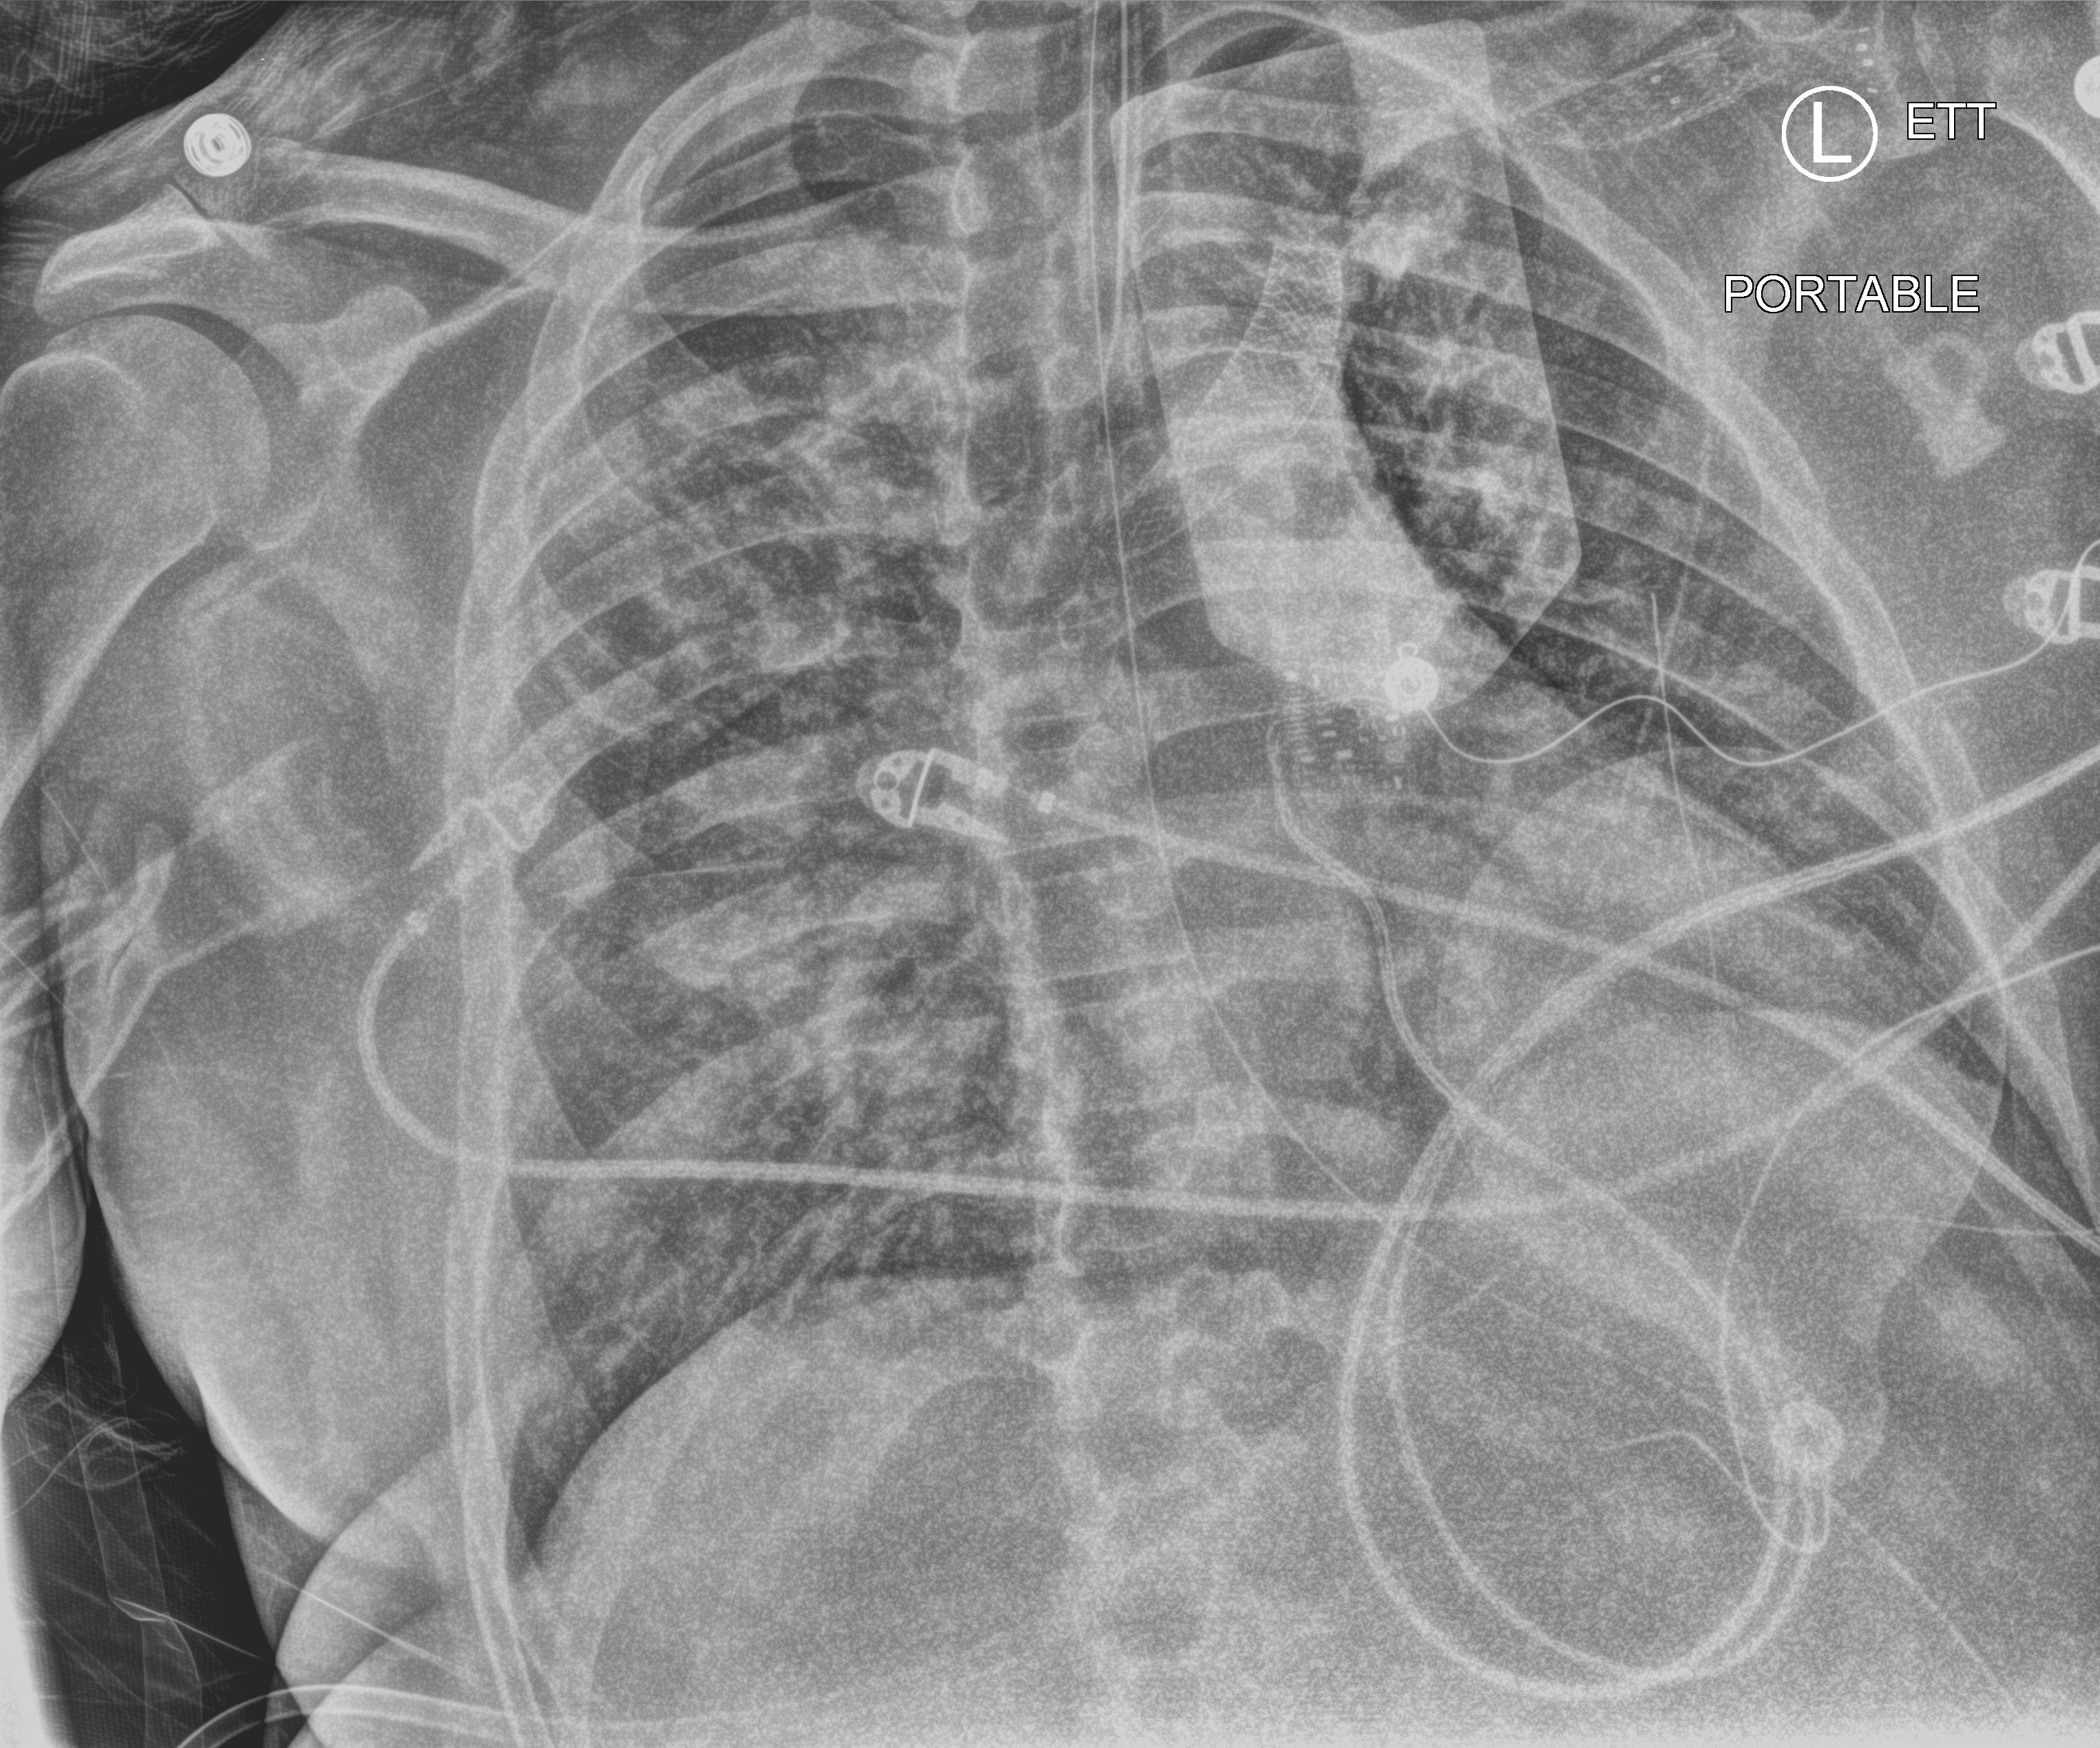
Portable chest radiograph; anteroposterior (AP) projection. Male patient hospitalised with COVID-19, age 18–59 years.
Admission-level facts for this patient (not findings on this image; timing relative to this image not recorded):
- mechanically ventilated during this hospital stay: yes
- diabetes (admission record): no
- chronic kidney disease (admission record): yes